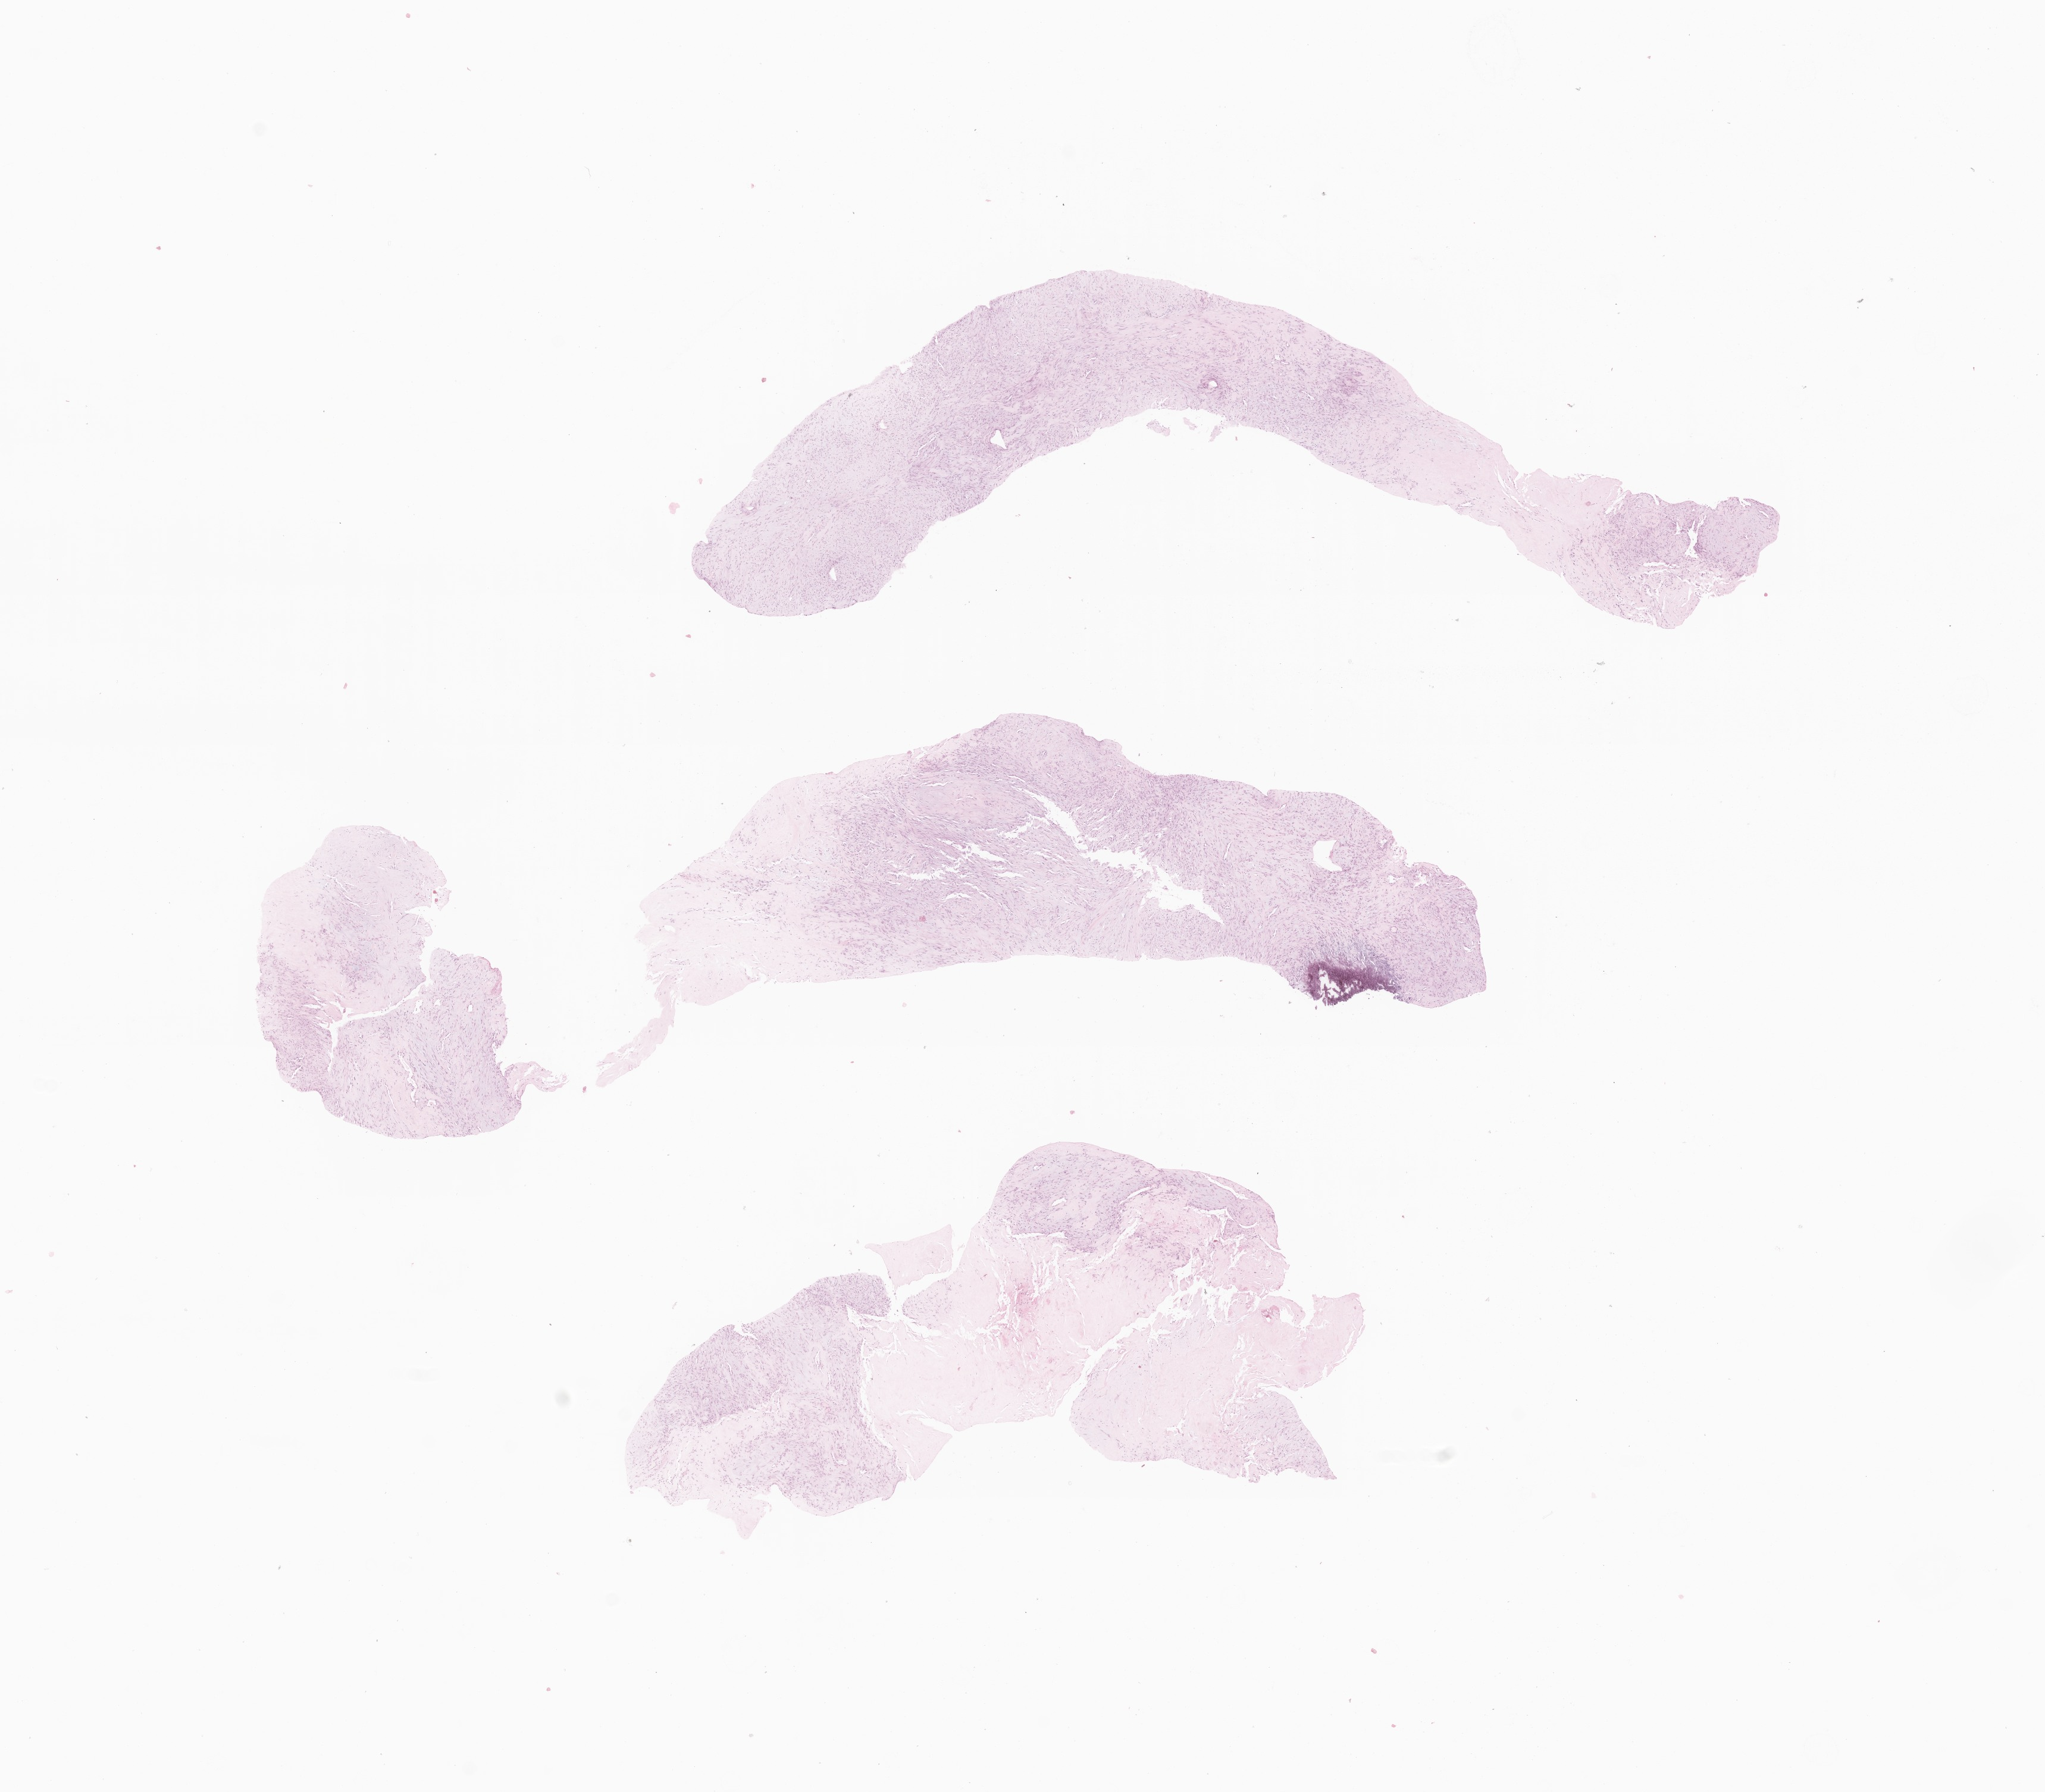
Digitized H&E-stained section of tumor tissue from the soft tissue of upper extremity — a low-resolution overview of the entire scanned area, about 14.5 x 12.7 mm, FFPE section. Patient: female, age 84 days.
Diagnosis: Spindle cell carcinoma, NOS.